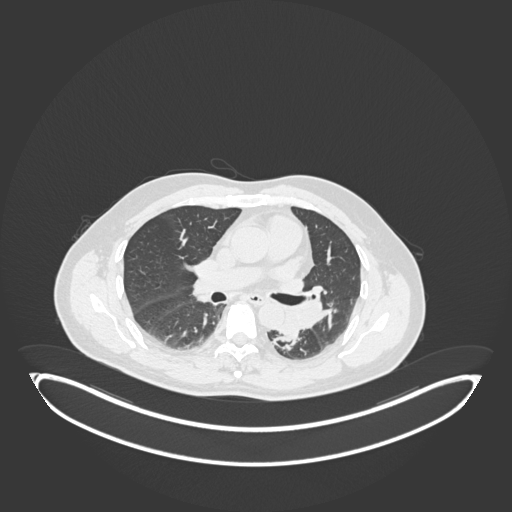
Chest CT, one axial slice. Position 114 of 258 along the scan axis. Lung window (W 1500 / L -600 HU). 1 mm slice thickness. 512 × 512 image matrix, field of view 500 × 500 mm. Patient: male, 54 years. From the clinical record (not read from this slice): clinical TNM (as recorded): T3 N0 M0.
Annotated regions visible in this slice (bounding box drawn by a radiologist):
- lung tumour (recorded histology: squamous cell carcinoma): box from (x=280, y=300) to (x=310, y=341) px